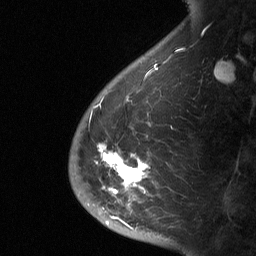
Breast MRI (dynamic contrast-enhanced), one sagittal slice; position 13 of 64 along the scan axis; dynamic contrast-enhanced study with each time point stored as its own series, time point 2 of 3 at this slice position (early post-contrast, ordered by acquisition time); 1.5 T; TE 4.8 ms, TR 27 ms; 2 mm slice thickness; 256 × 256 image matrix, field of view 180 × 180 mm. Female patient, age 56 years. Case-level facts recorded for this patient, not image findings: setting: breast cancer imaged before/during neoadjuvant chemotherapy; receptor status: HER2-positive.
Annotated regions visible in this slice (semi-automatically segmented with operator editing):
- analysis volume of interest (the breast-tissue region the enhancement analysis was run in; not a lesion): bounding box (x1, y1, x2, y2) in pixels: (68, 140, 182, 229)
- tumour enhancement mask (voxels above the 90 % enhancement threshold inside the analysis volume of interest): (96, 143, 149, 227)